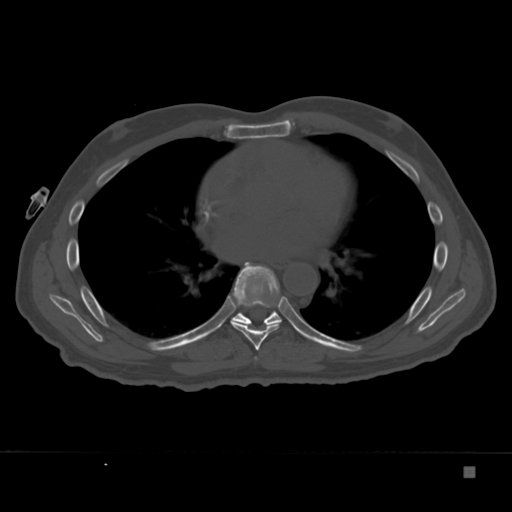
CT including the spine, one axial slice; slice 217 of 332 in the series (ordered by position); 120 kVp; bone window (W 1800 / L 400 HU); 1.5 mm slice thickness; 512 × 512 image matrix. Patient: male, 72 years. From the clinical record (not read from this slice): primary cancer: skeletal.
Outlined on this slice (semi-automatic segmentation, software-assisted and operator-edited):
- T6 vertebra: bounding box (x1, y1, x2, y2) in pixels: (255, 357, 257, 359)
- T7 vertebra: (230, 262, 282, 351)
- T8 vertebra: (232, 302, 301, 334)